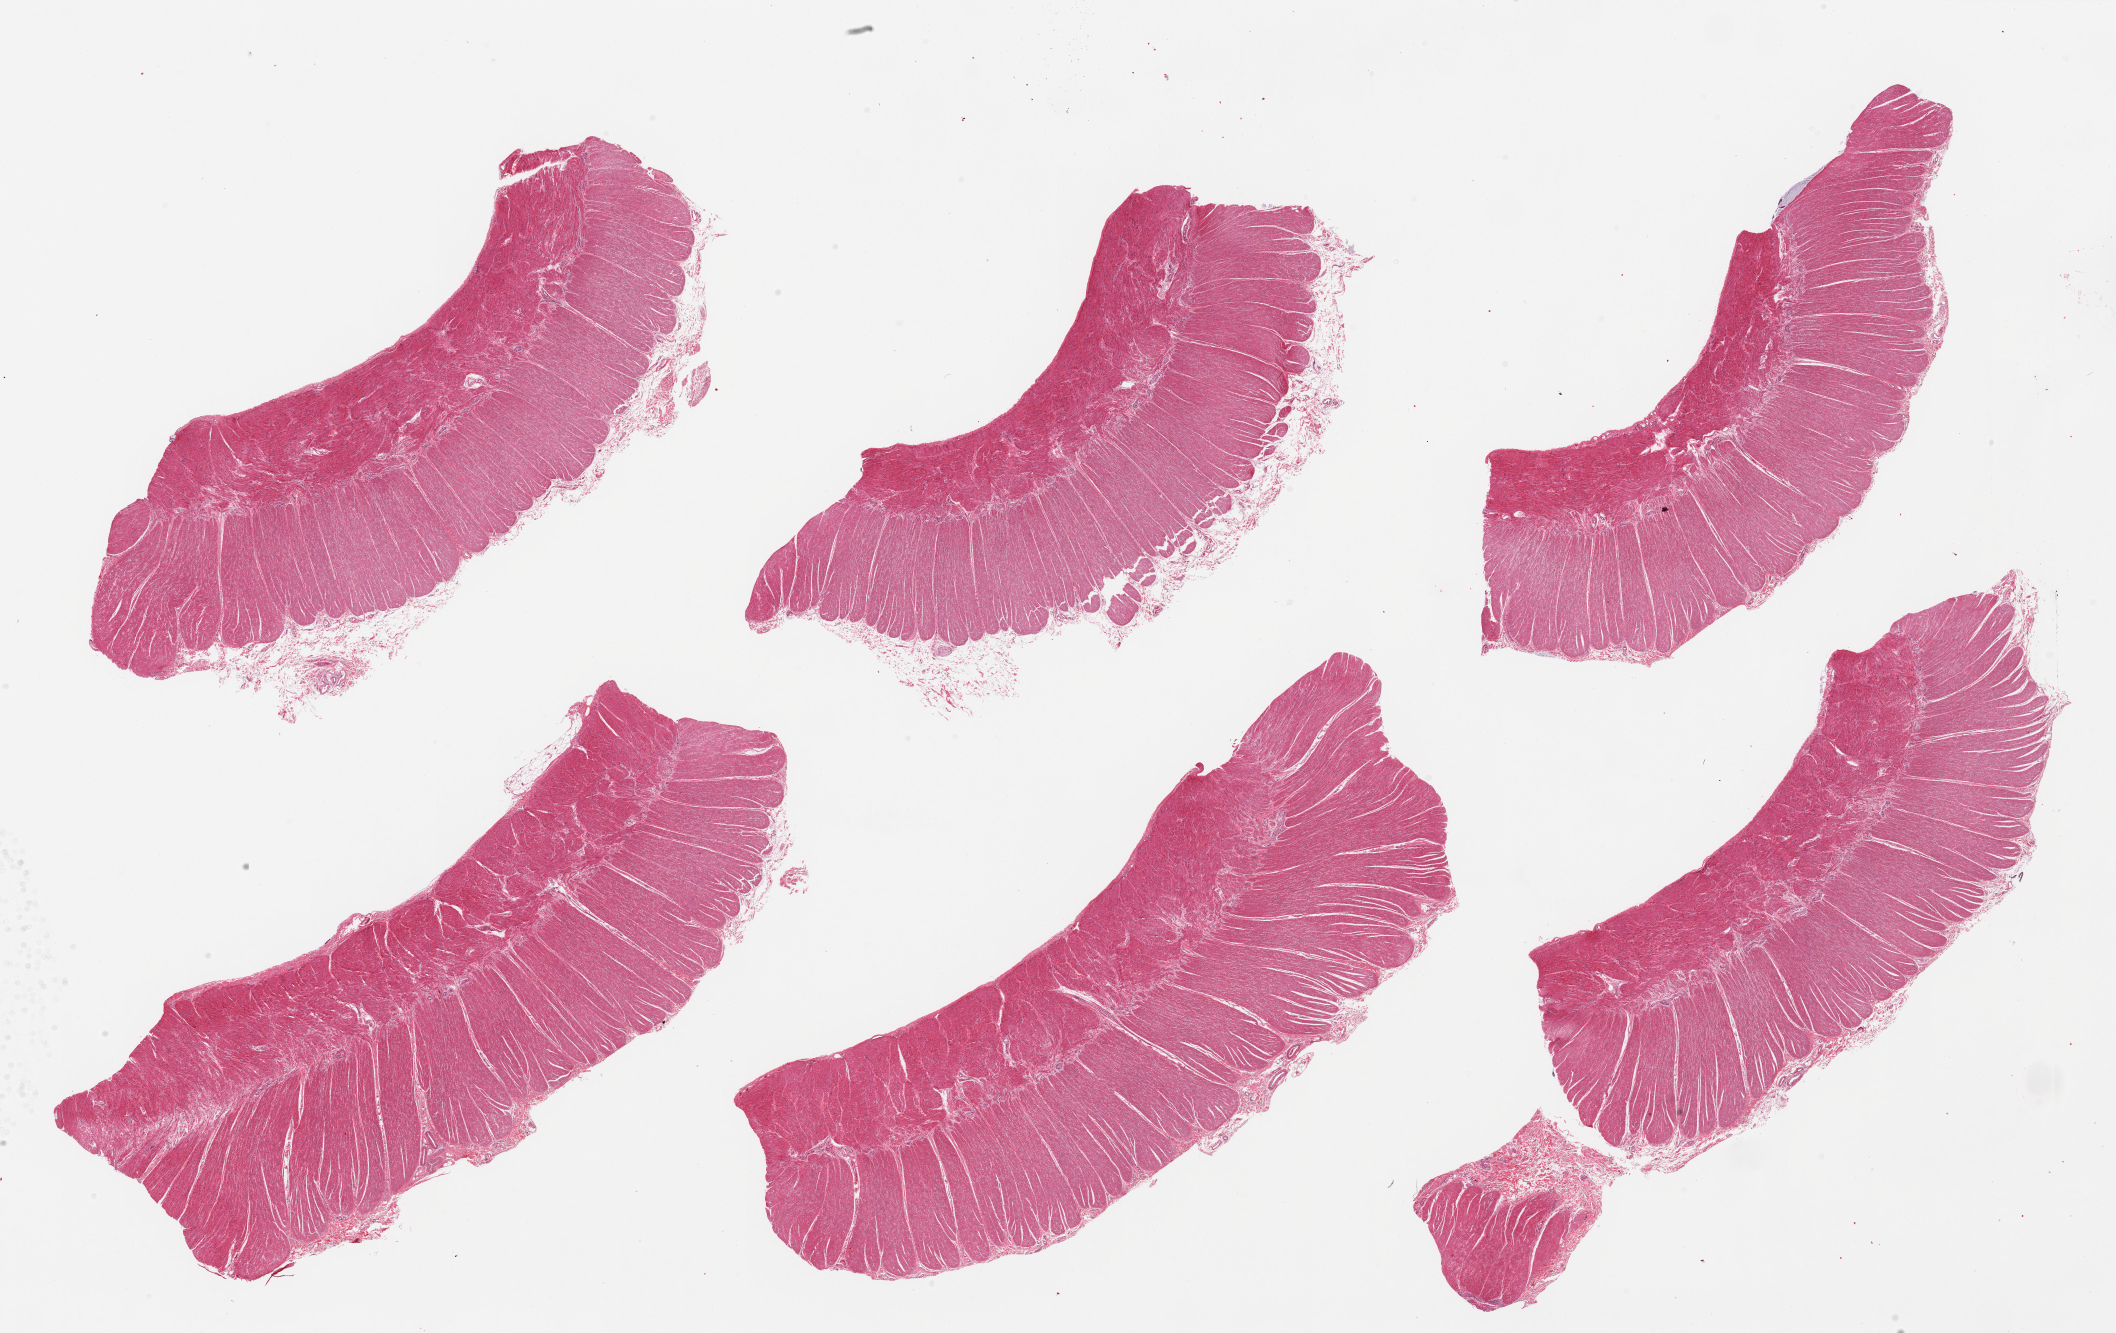
Hematoxylin and eosin (H&E) whole-slide image, shown as a low-resolution overview of the whole scanned area (about 33.5 x 21.1 mm). PAXgene-fixed, paraffin-embedded tissue. Sampled site (target tissue): sigmoid colon. Tissue donor sample. Donor sex: male.
* pathologist's review note for this sample: 6 pieces; well dissected muscularis propria